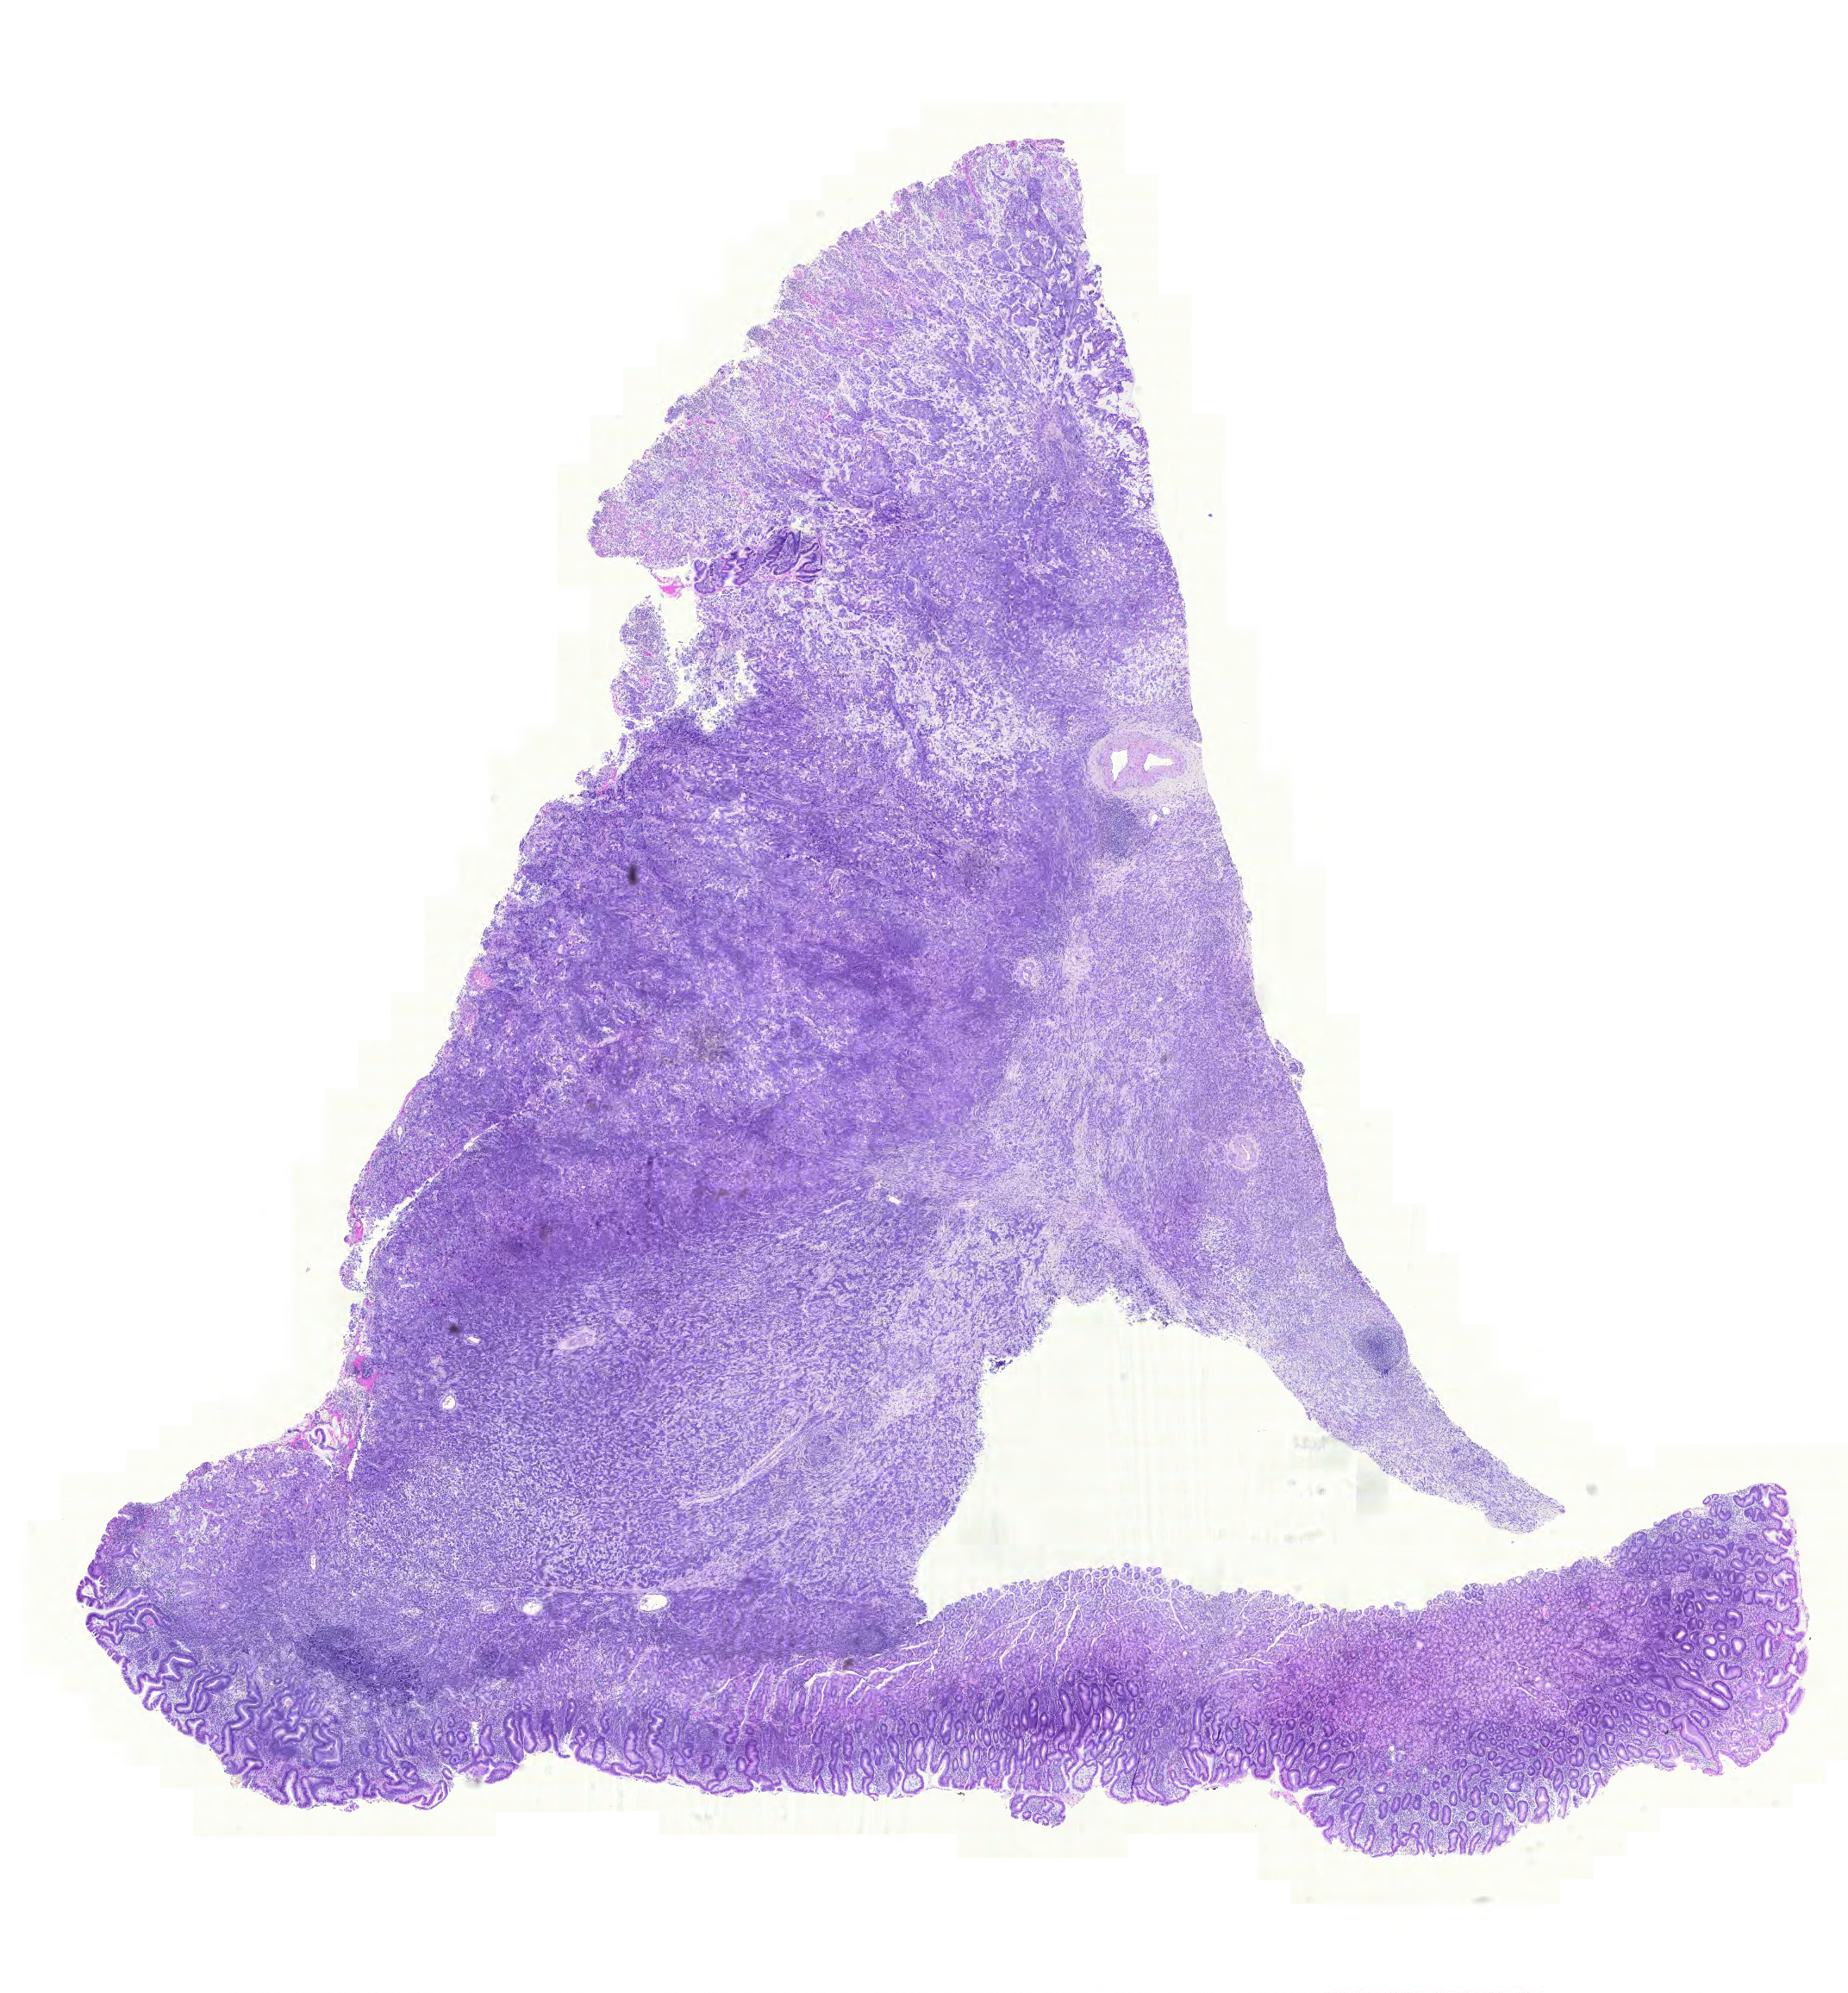
H&E whole-slide image, whole scanned area (about 16.0 x 17.2 mm, slide scanned at 20x) shown as a low-resolution overview; formalin-fixed paraffin-embedded (FFPE) diagnostic section; primary tumour sample from the stomach. Patient: female, age at initial diagnosis 69 years.
Histologic diagnosis: Carcinoma, diffuse type (gastric antrum).